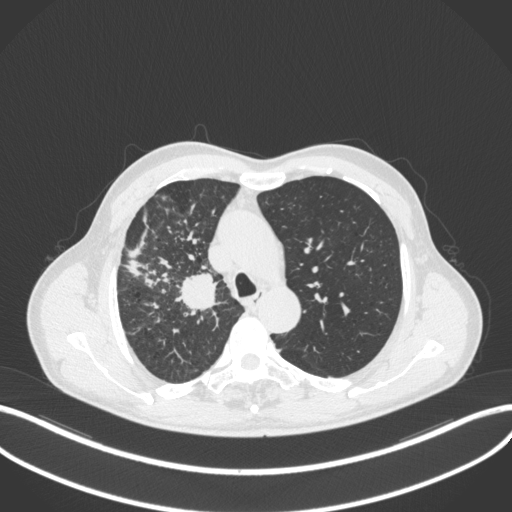
Chest CT, one axial slice; slice 347 of 490 in the series (ordered by position); reconstruction kernel B31f; 120 kVp; lung window (W 1500 / L -600 HU); 1 mm slice thickness; 512 × 512 image matrix, field of view 400 × 400 mm. Patient: male, 69 years. Case-level facts recorded for this patient, not image findings: clinical TNM (as recorded): T2a N0 M0.
Annotated regions visible in this slice (rectangle marked by the reading radiologist):
- lung tumour (recorded histology: adenocarcinoma): box from (x=174, y=272) to (x=223, y=314) px